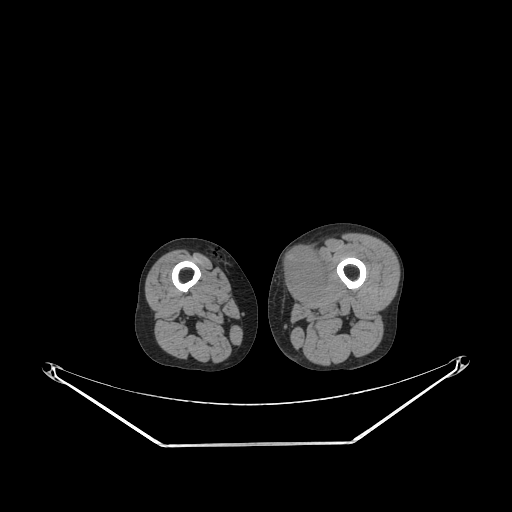
CT of an extremity soft-tissue mass (from a PET/CT study), one axial slice; slice 216 of 267 in the series (ordered by position); 140 kVp; soft-tissue window (W 400 / L 40 HU); 3.75 mm slice thickness; 512 × 512 image matrix, field of view 500 × 500 mm. Male patient. From the clinical record (not read from this slice): histological type: pleiomorphic leiomyosarcoma; grade: high; site of the primary tumour: left thigh.
Structures marked on this image (expert contour drawn on MRI and transferred to this co-registered scan by the dataset authors):
- gross tumour volume including surrounding oedema: bounding box [x1, y1, x2, y2] px = [279, 247, 330, 300]
- gross tumour volume (mass): [279, 249, 325, 300]